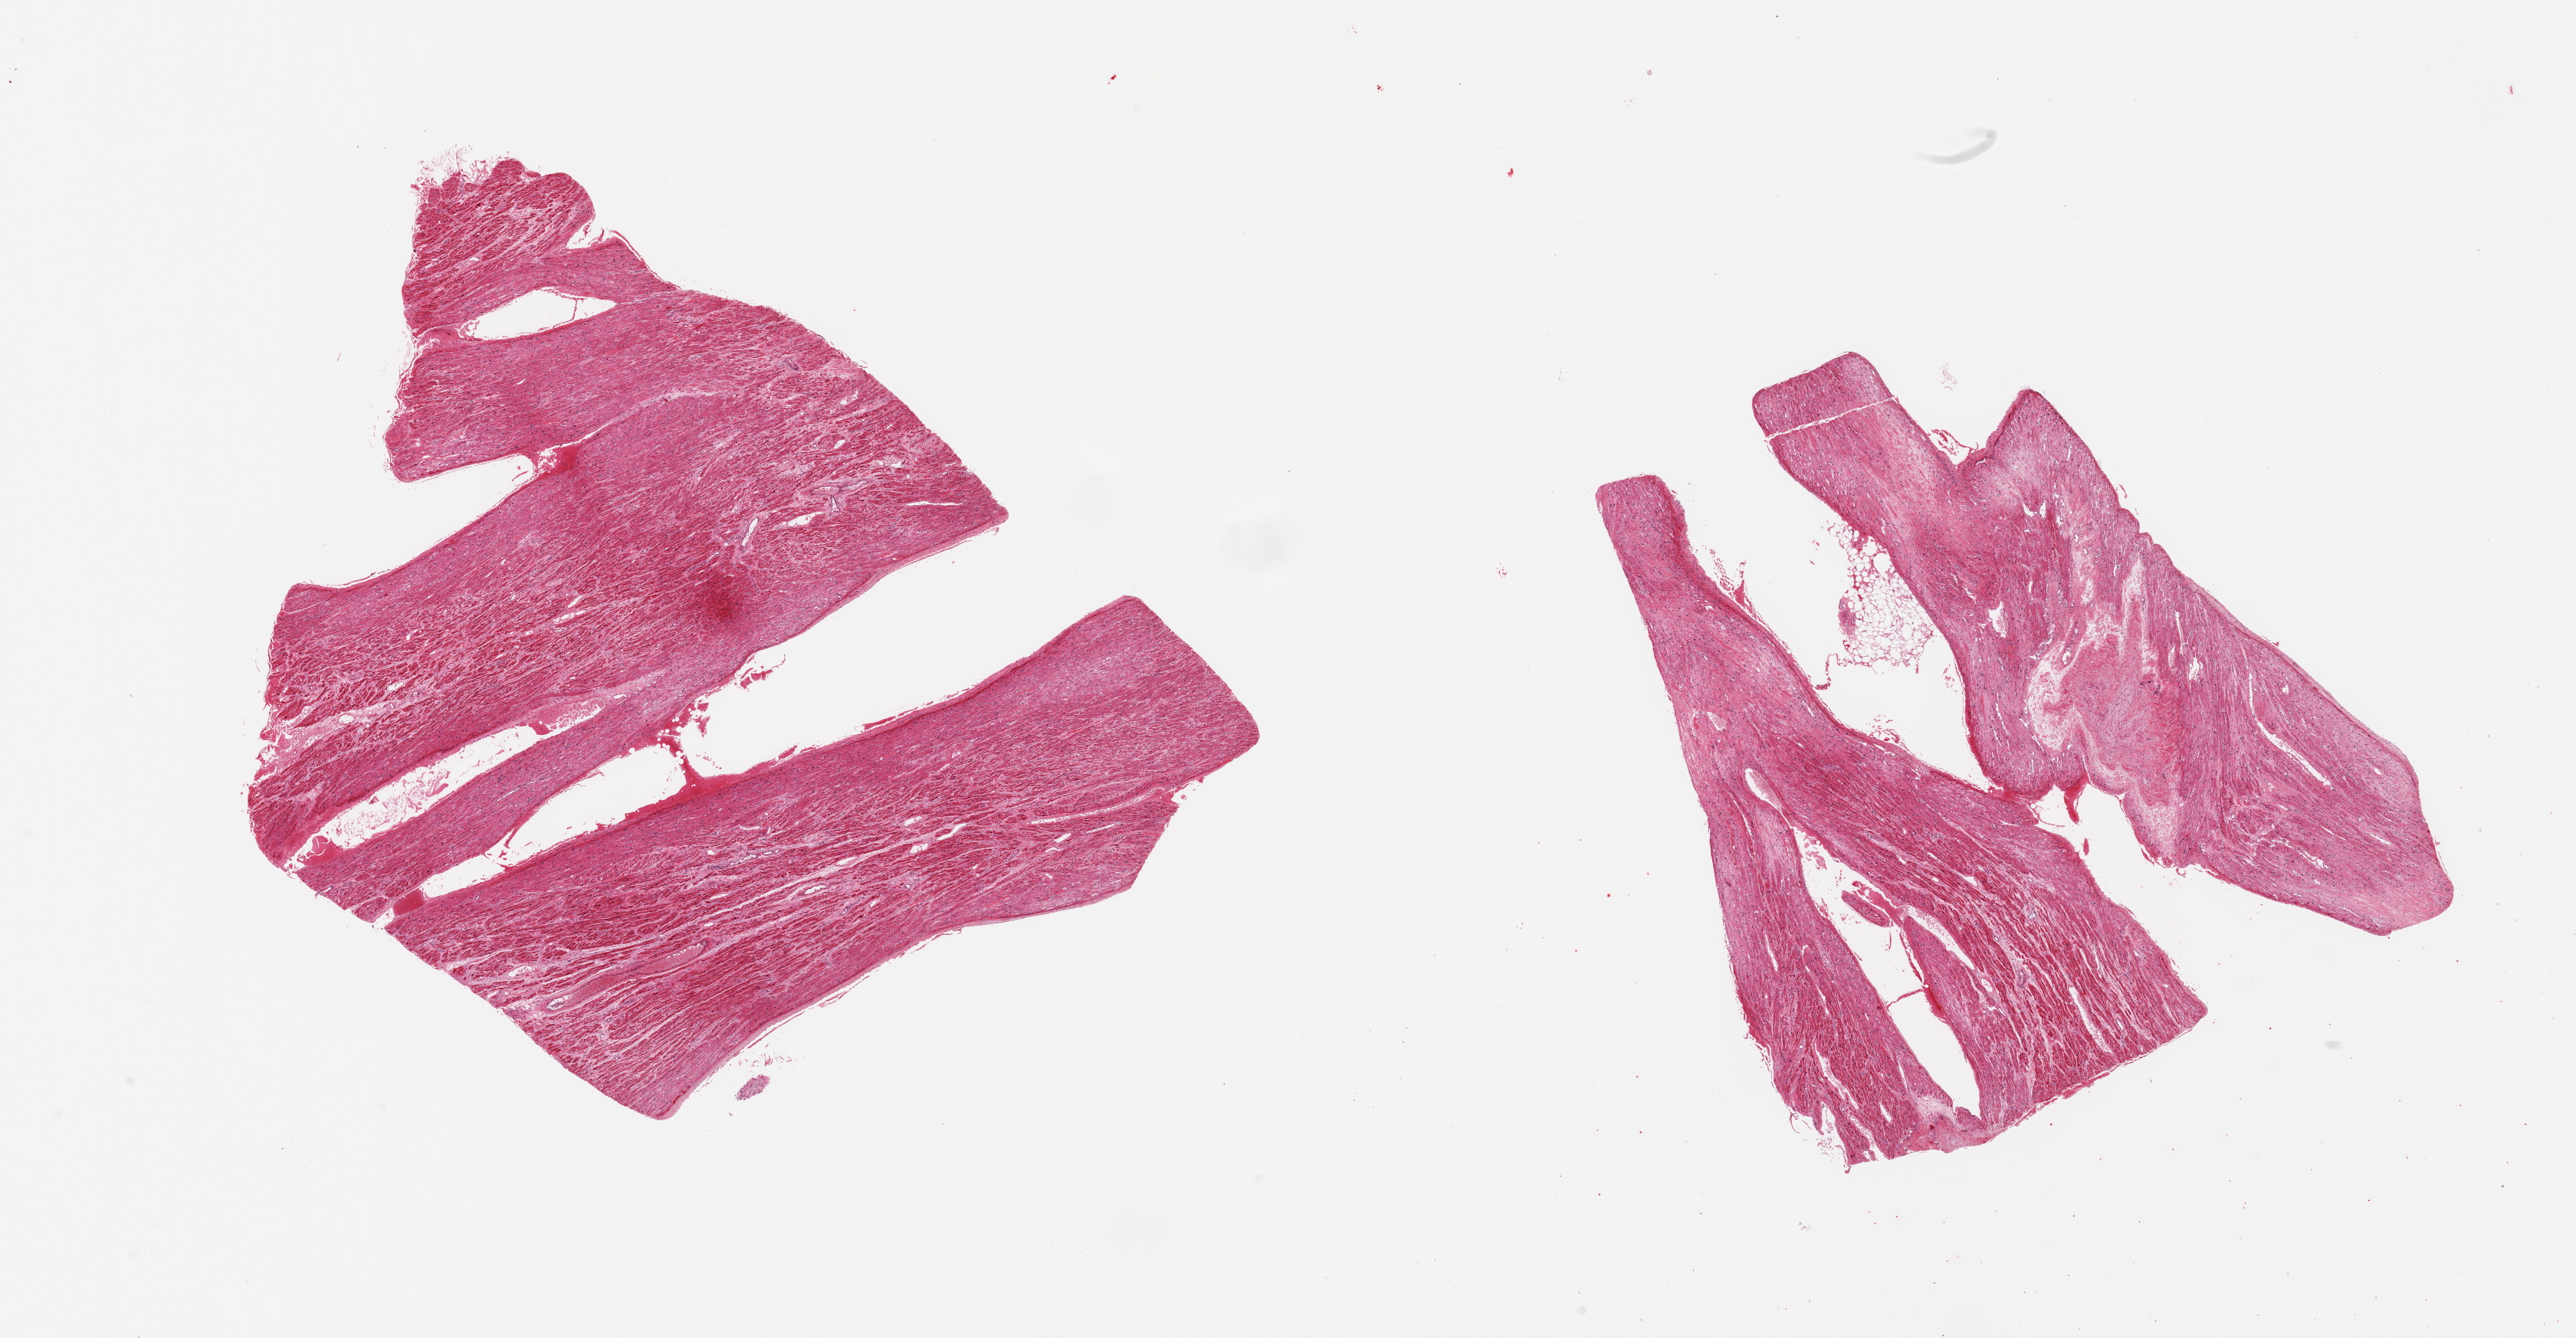
Whole-slide image, hematoxylin and eosin (H&E) stain — low-resolution overview of the scanned area, about 26.6 x 13.8 mm (slide scanned at 20x), PAXgene-fixed, paraffin-embedded tissue, target tissue: auricular appendage, donor tissue sample.
Review note (as recorded): 2 pieces; patchy interstitial fibrosis and hypereosinophilia suggesting old and recent ischemia.